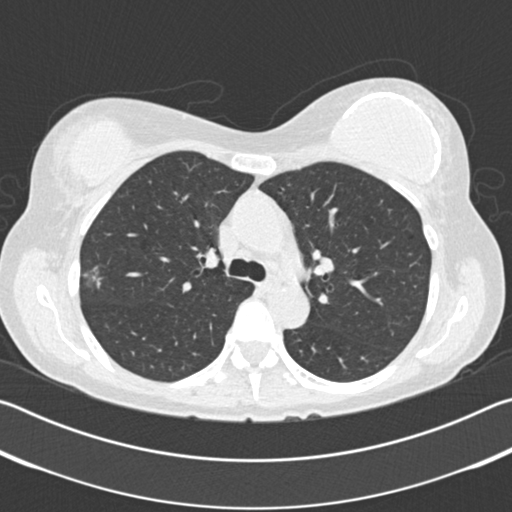
Low-dose screening chest CT, one axial slice; position 125 of 183 along the scan axis; reconstruction kernel B30f; 120 kVp; lung window (W 1500 / L -600 HU); 2 mm slice thickness; 512 × 512 image matrix, field of view 340 × 340 mm.
Outlined on this slice (manually delineated by an expert):
- lesion 1 (tumor, upper lobe of right lung): bounding box [x1, y1, x2, y2] px = [85, 272, 100, 287]